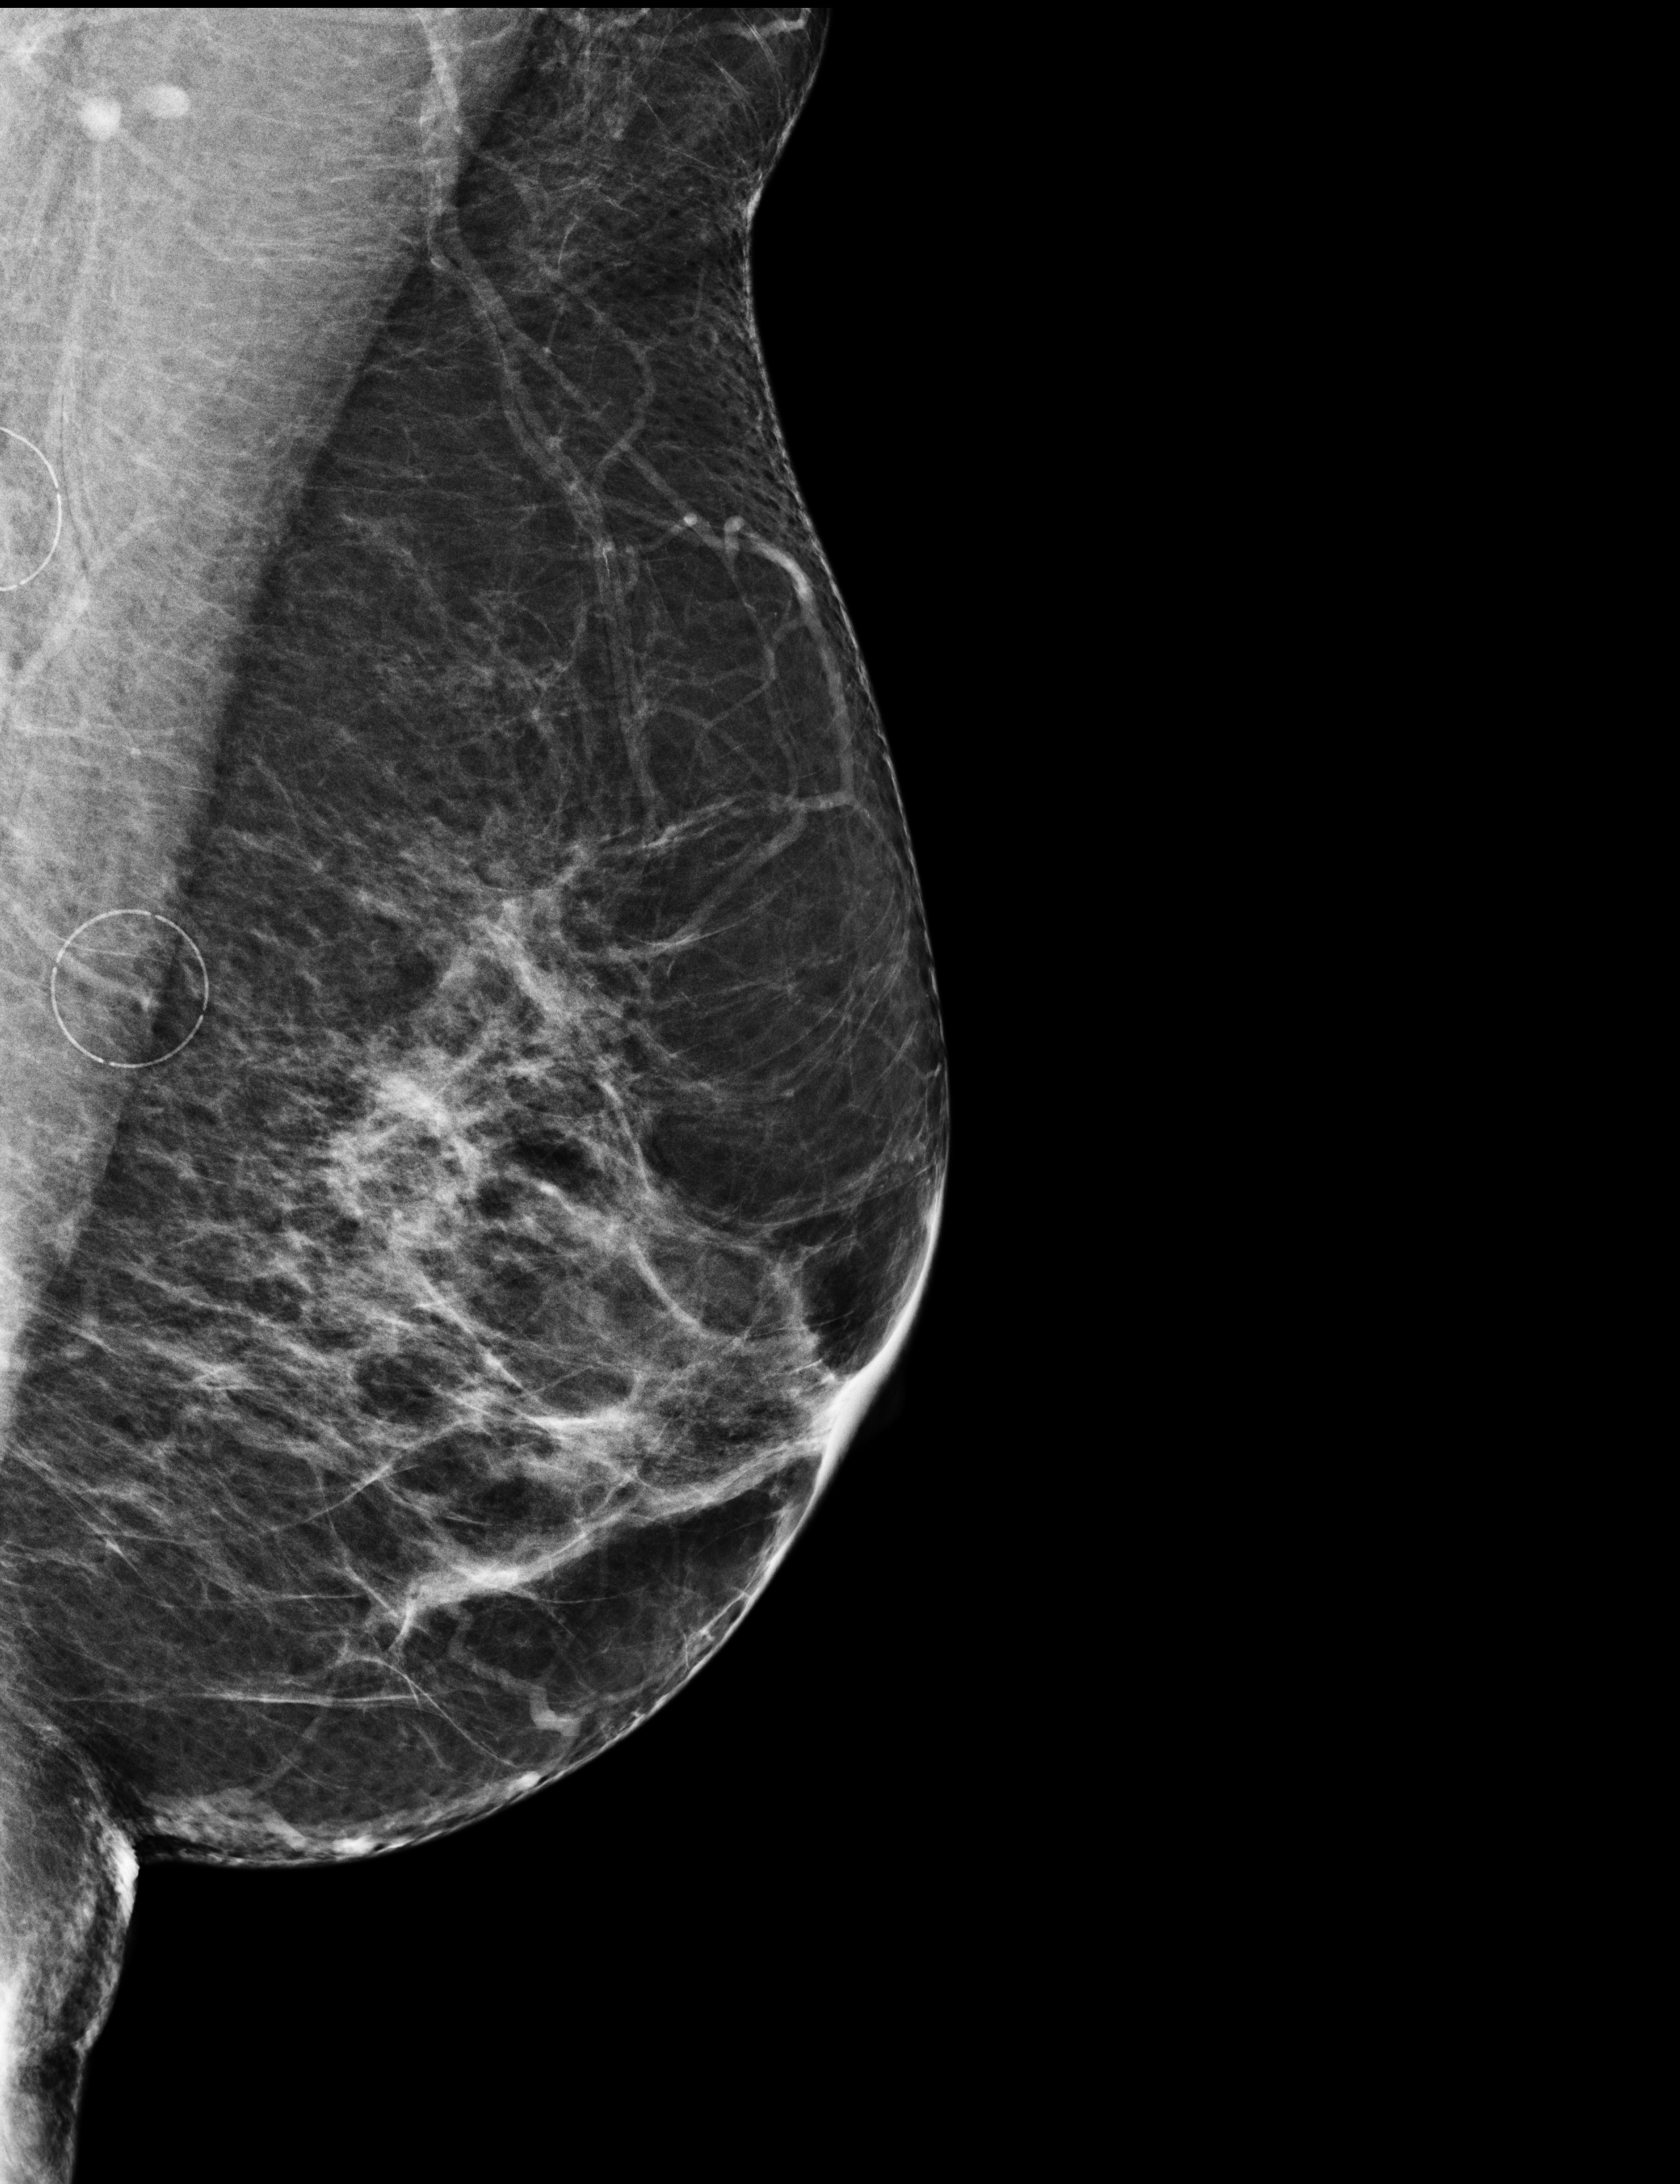
Screening examination. Patient: female, 61 years.
Image type: full-field digital mammogram. Breast: left. Projection: mediolateral oblique (MLO) view.